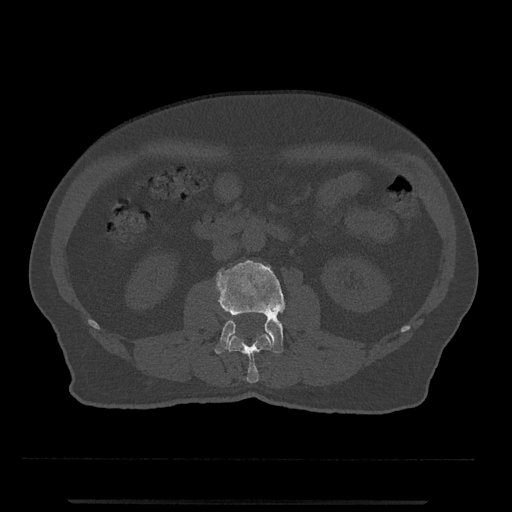
CT including the spine, one axial slice; slice 229 of 797 in the series (ordered by position); reconstruction kernel Br40s/3; bone window (W 1800 / L 400 HU); 512 × 512 image matrix, field of view 419 × 419 mm. Male patient, age 63 years. From the clinical record (not read from this slice): primary cancer: prostate.
Annotated regions visible in this slice (semi-automatic segmentation, software-assisted and operator-edited):
- L2 vertebra: bounding box (x1, y1, x2, y2) in pixels: (226, 333, 273, 383)
- L3 vertebra: (215, 259, 286, 354)